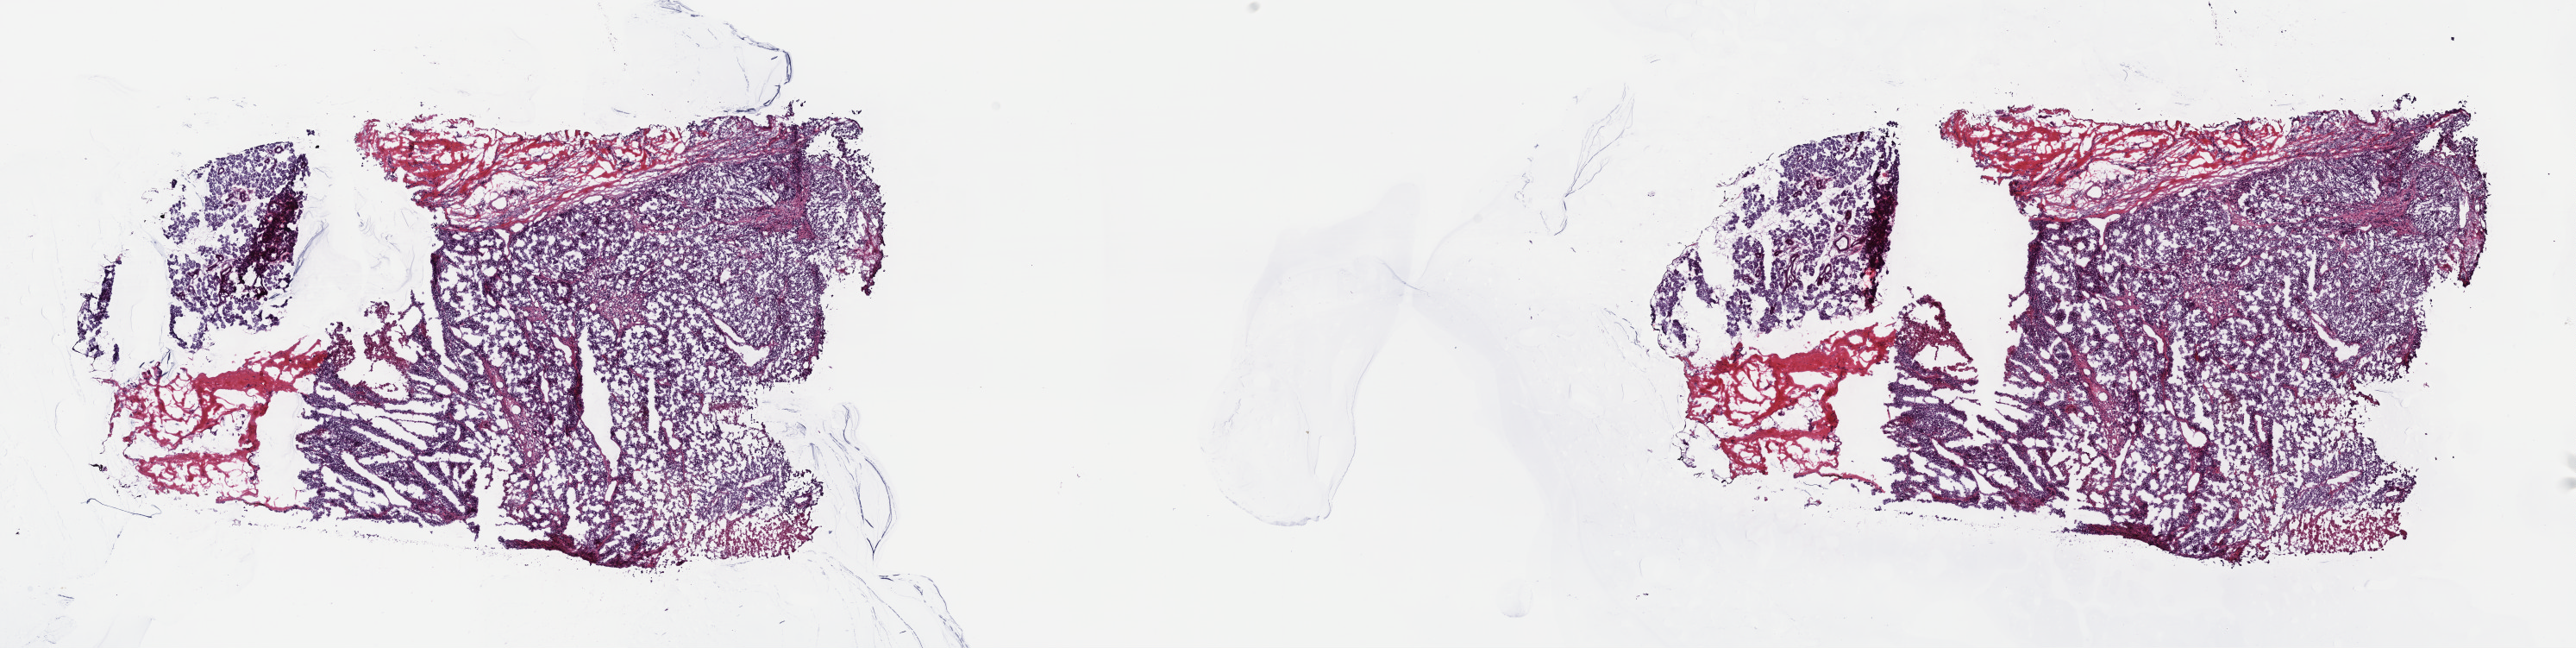
Whole-slide histology image, H&E — low-resolution overview of the scanned area, about 24.2 x 6.1 mm (from a 40x scan); frozen section from the top of the tissue portion; metastatic tumour sample. Patient: male, age at initial diagnosis 82 years. Composition of this section per pathologist review: tumour cells 80%, tumour nuclei 80%, normal cells 0%, stromal cells 20%, necrosis 0%. Inflammatory infiltration, as recorded: lymphocyte infiltration 2%, monocyte infiltration 1%, neutrophil infiltration 1%.
This section: metastatic tumour tissue. Patient diagnosis: Malignant melanoma, NOS.